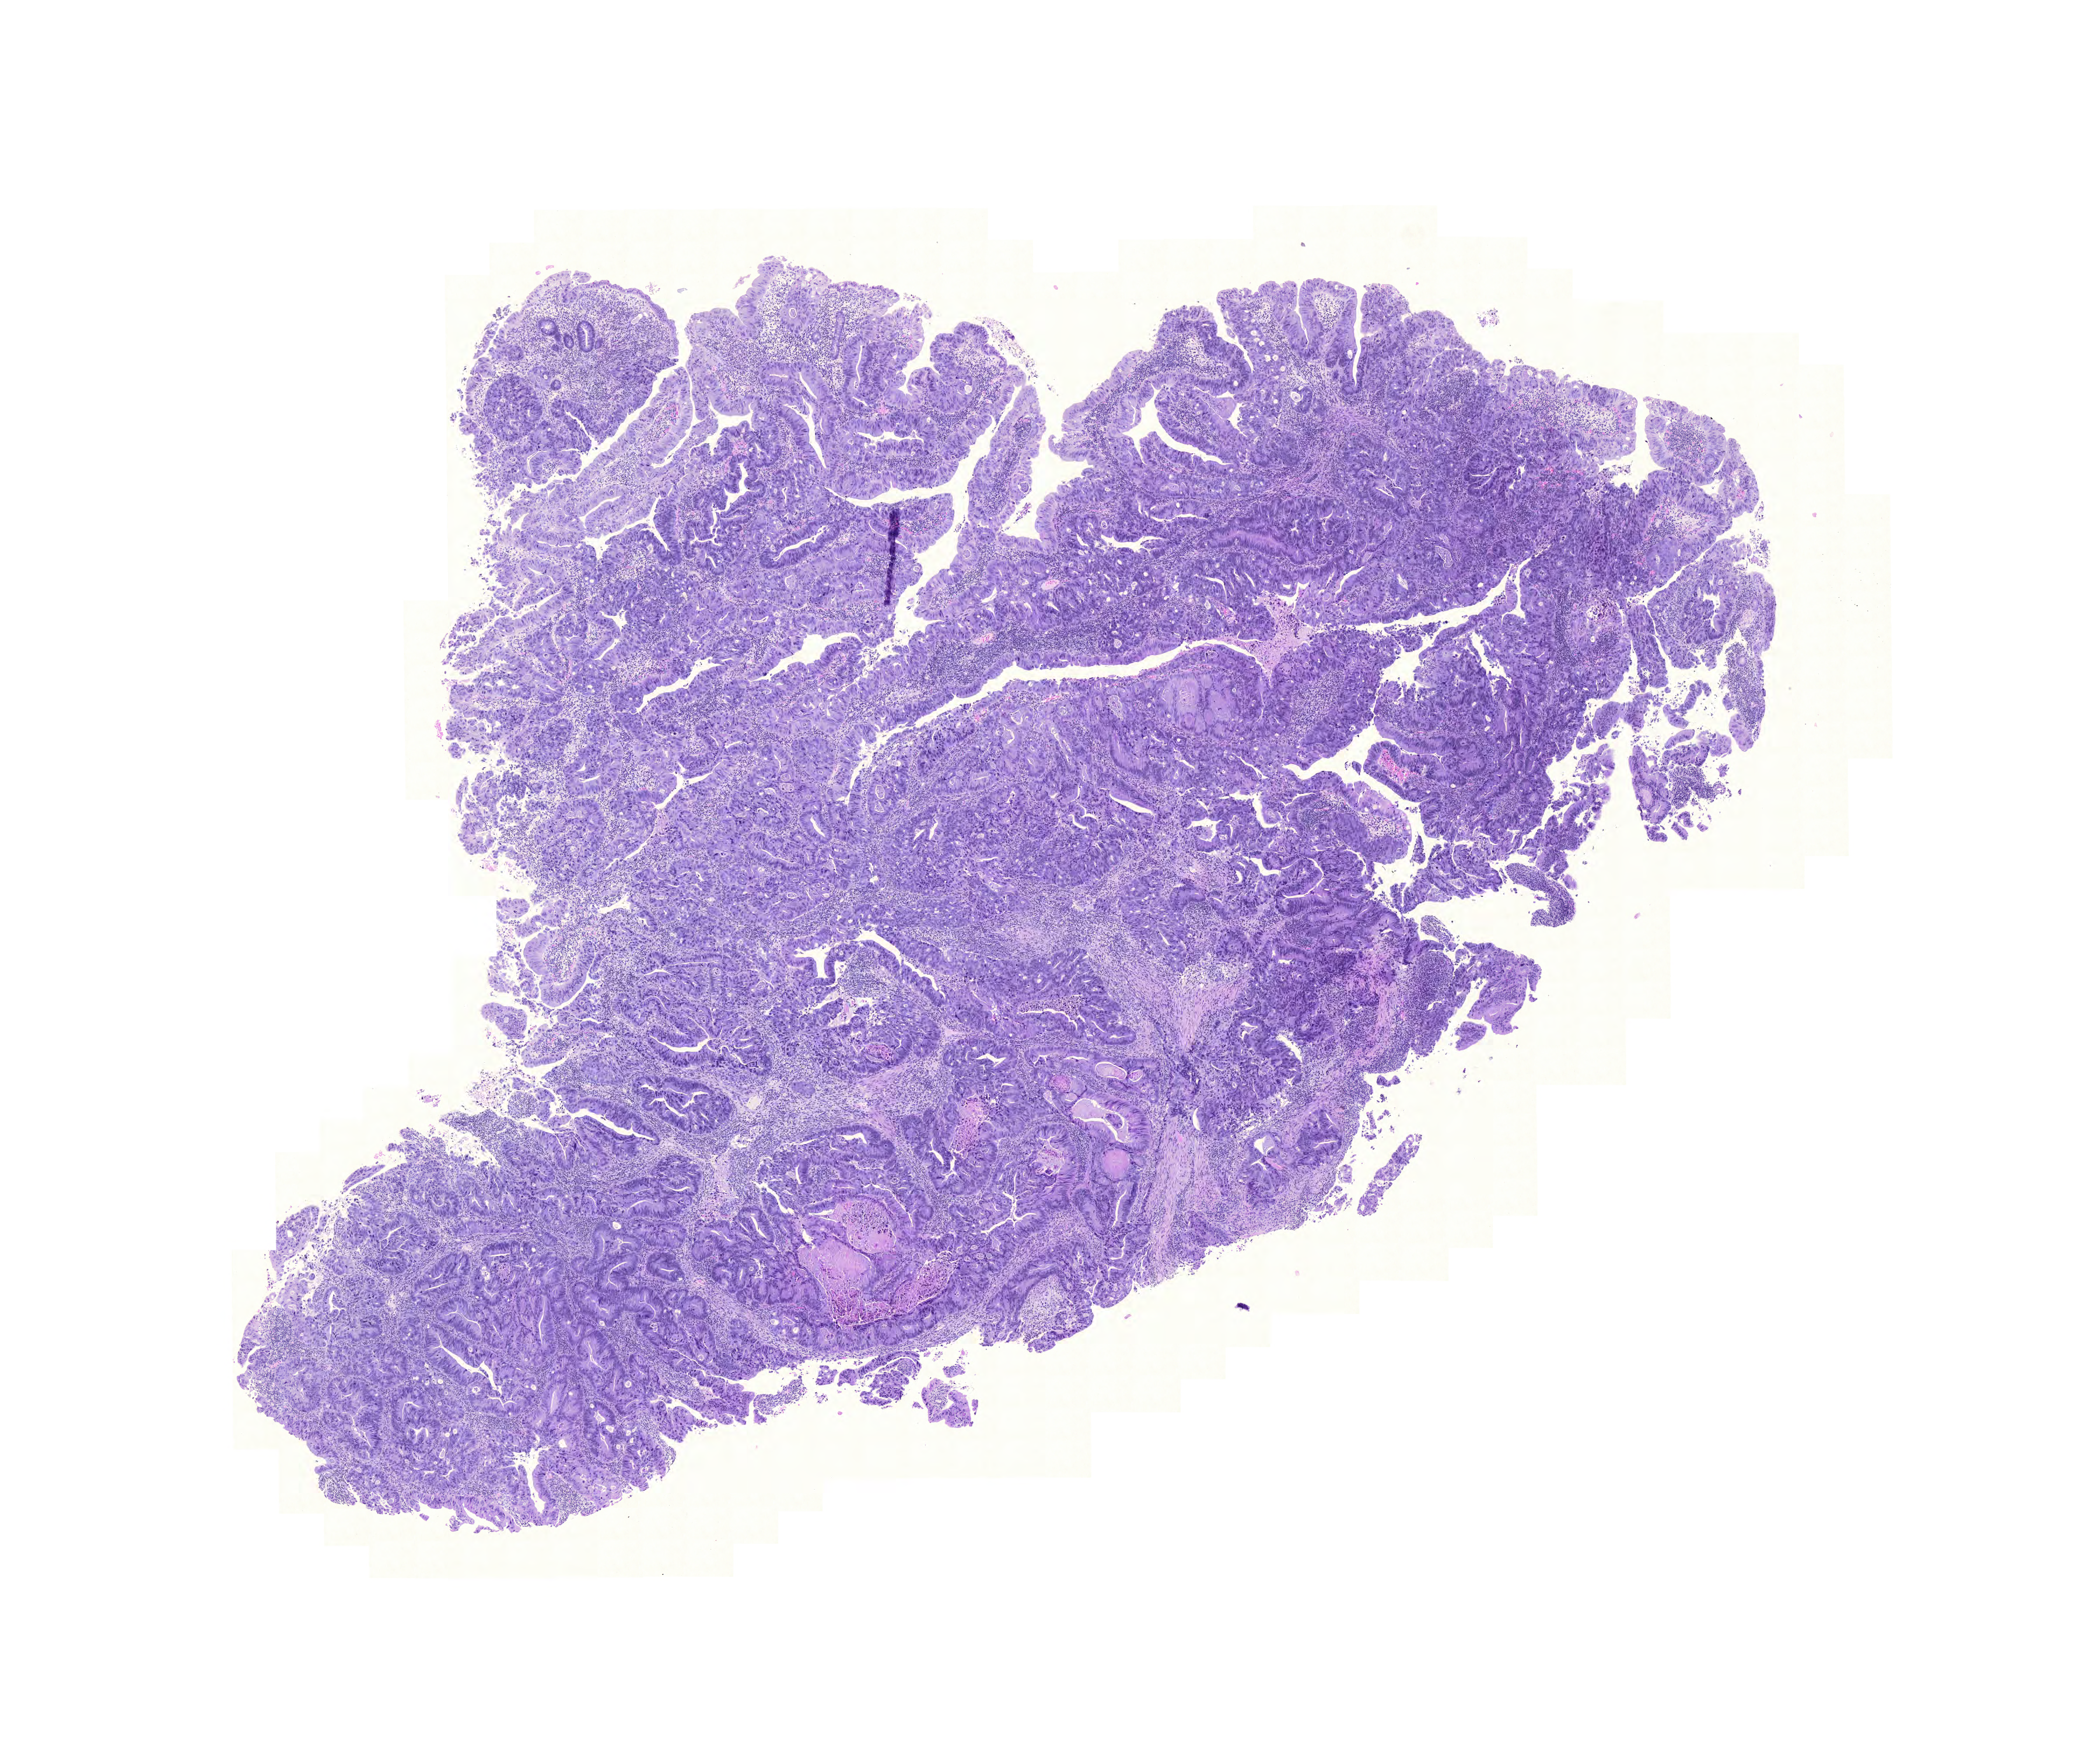
Whole-slide histology image, Hematoxylin and eosin (H&E) stained — low-resolution overview of the scanned area, about 13.4 x 11.1 mm; formalin-fixed paraffin-embedded (FFPE) diagnostic section; colon, primary tumour sample. Patient: male, age at initial diagnosis 85 years.
- AJCC pathologic stage: IIIC (6th edition)
- TNM: T3 N2 M0
- histologic diagnosis: Adenocarcinoma, NOS (cecum)
- lymph nodes positive (case pathology): 10 of 20 examined